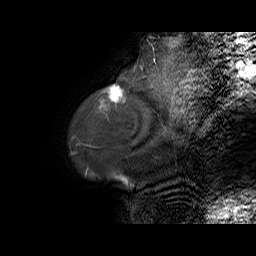
Breast MRI (dynamic contrast-enhanced), one sagittal slice; position 9 of 70 along the scan axis; dynamic contrast-enhanced series, time point 2 of 6 at this slice position (early post-contrast); 1.5 T; TE 5.5 ms, TR 32.9 ms; 4 mm slice thickness; 256 × 256 image matrix, field of view 240 × 240 mm. Female patient. Case-level facts recorded for this patient, not image findings: setting: breast cancer imaged before/during neoadjuvant chemotherapy; receptor status: HER2-positive.
Annotated regions visible in this slice (semi-automatic segmentation, software-assisted and operator-edited):
- analysis volume of interest (the breast-tissue region the enhancement analysis was run in; not a lesion): box from (x=99, y=79) to (x=141, y=108) px
- tumour enhancement mask (voxels above the 100 % enhancement threshold inside the analysis volume of interest): (x=109, y=86)–(x=125, y=102)